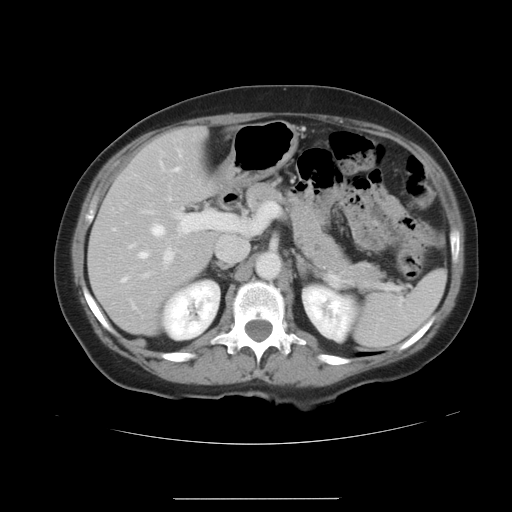
Contrast-enhanced abdominal CT, one axial slice; position 22 of 41 along the scan axis; intravenous contrast given; soft-tissue window (W 400 / L 40 HU); 512 × 512 image matrix, field of view 381 × 381 mm. Female patient, age 63 years. From the clinical record (not read from this slice): diagnosis: colorectal cancer liver metastases, imaged before liver resection.
Annotated regions visible in this slice (expert manual segmentation):
- hepatic veins: box from (x=122, y=168) to (x=179, y=282) px
- liver: (x=90, y=128)–(x=219, y=335)
- planned liver remnant (the part of the liver to remain after resection): (x=90, y=128)–(x=219, y=335)
- portal vein (with intrahepatic branches): (x=145, y=212)–(x=224, y=276)